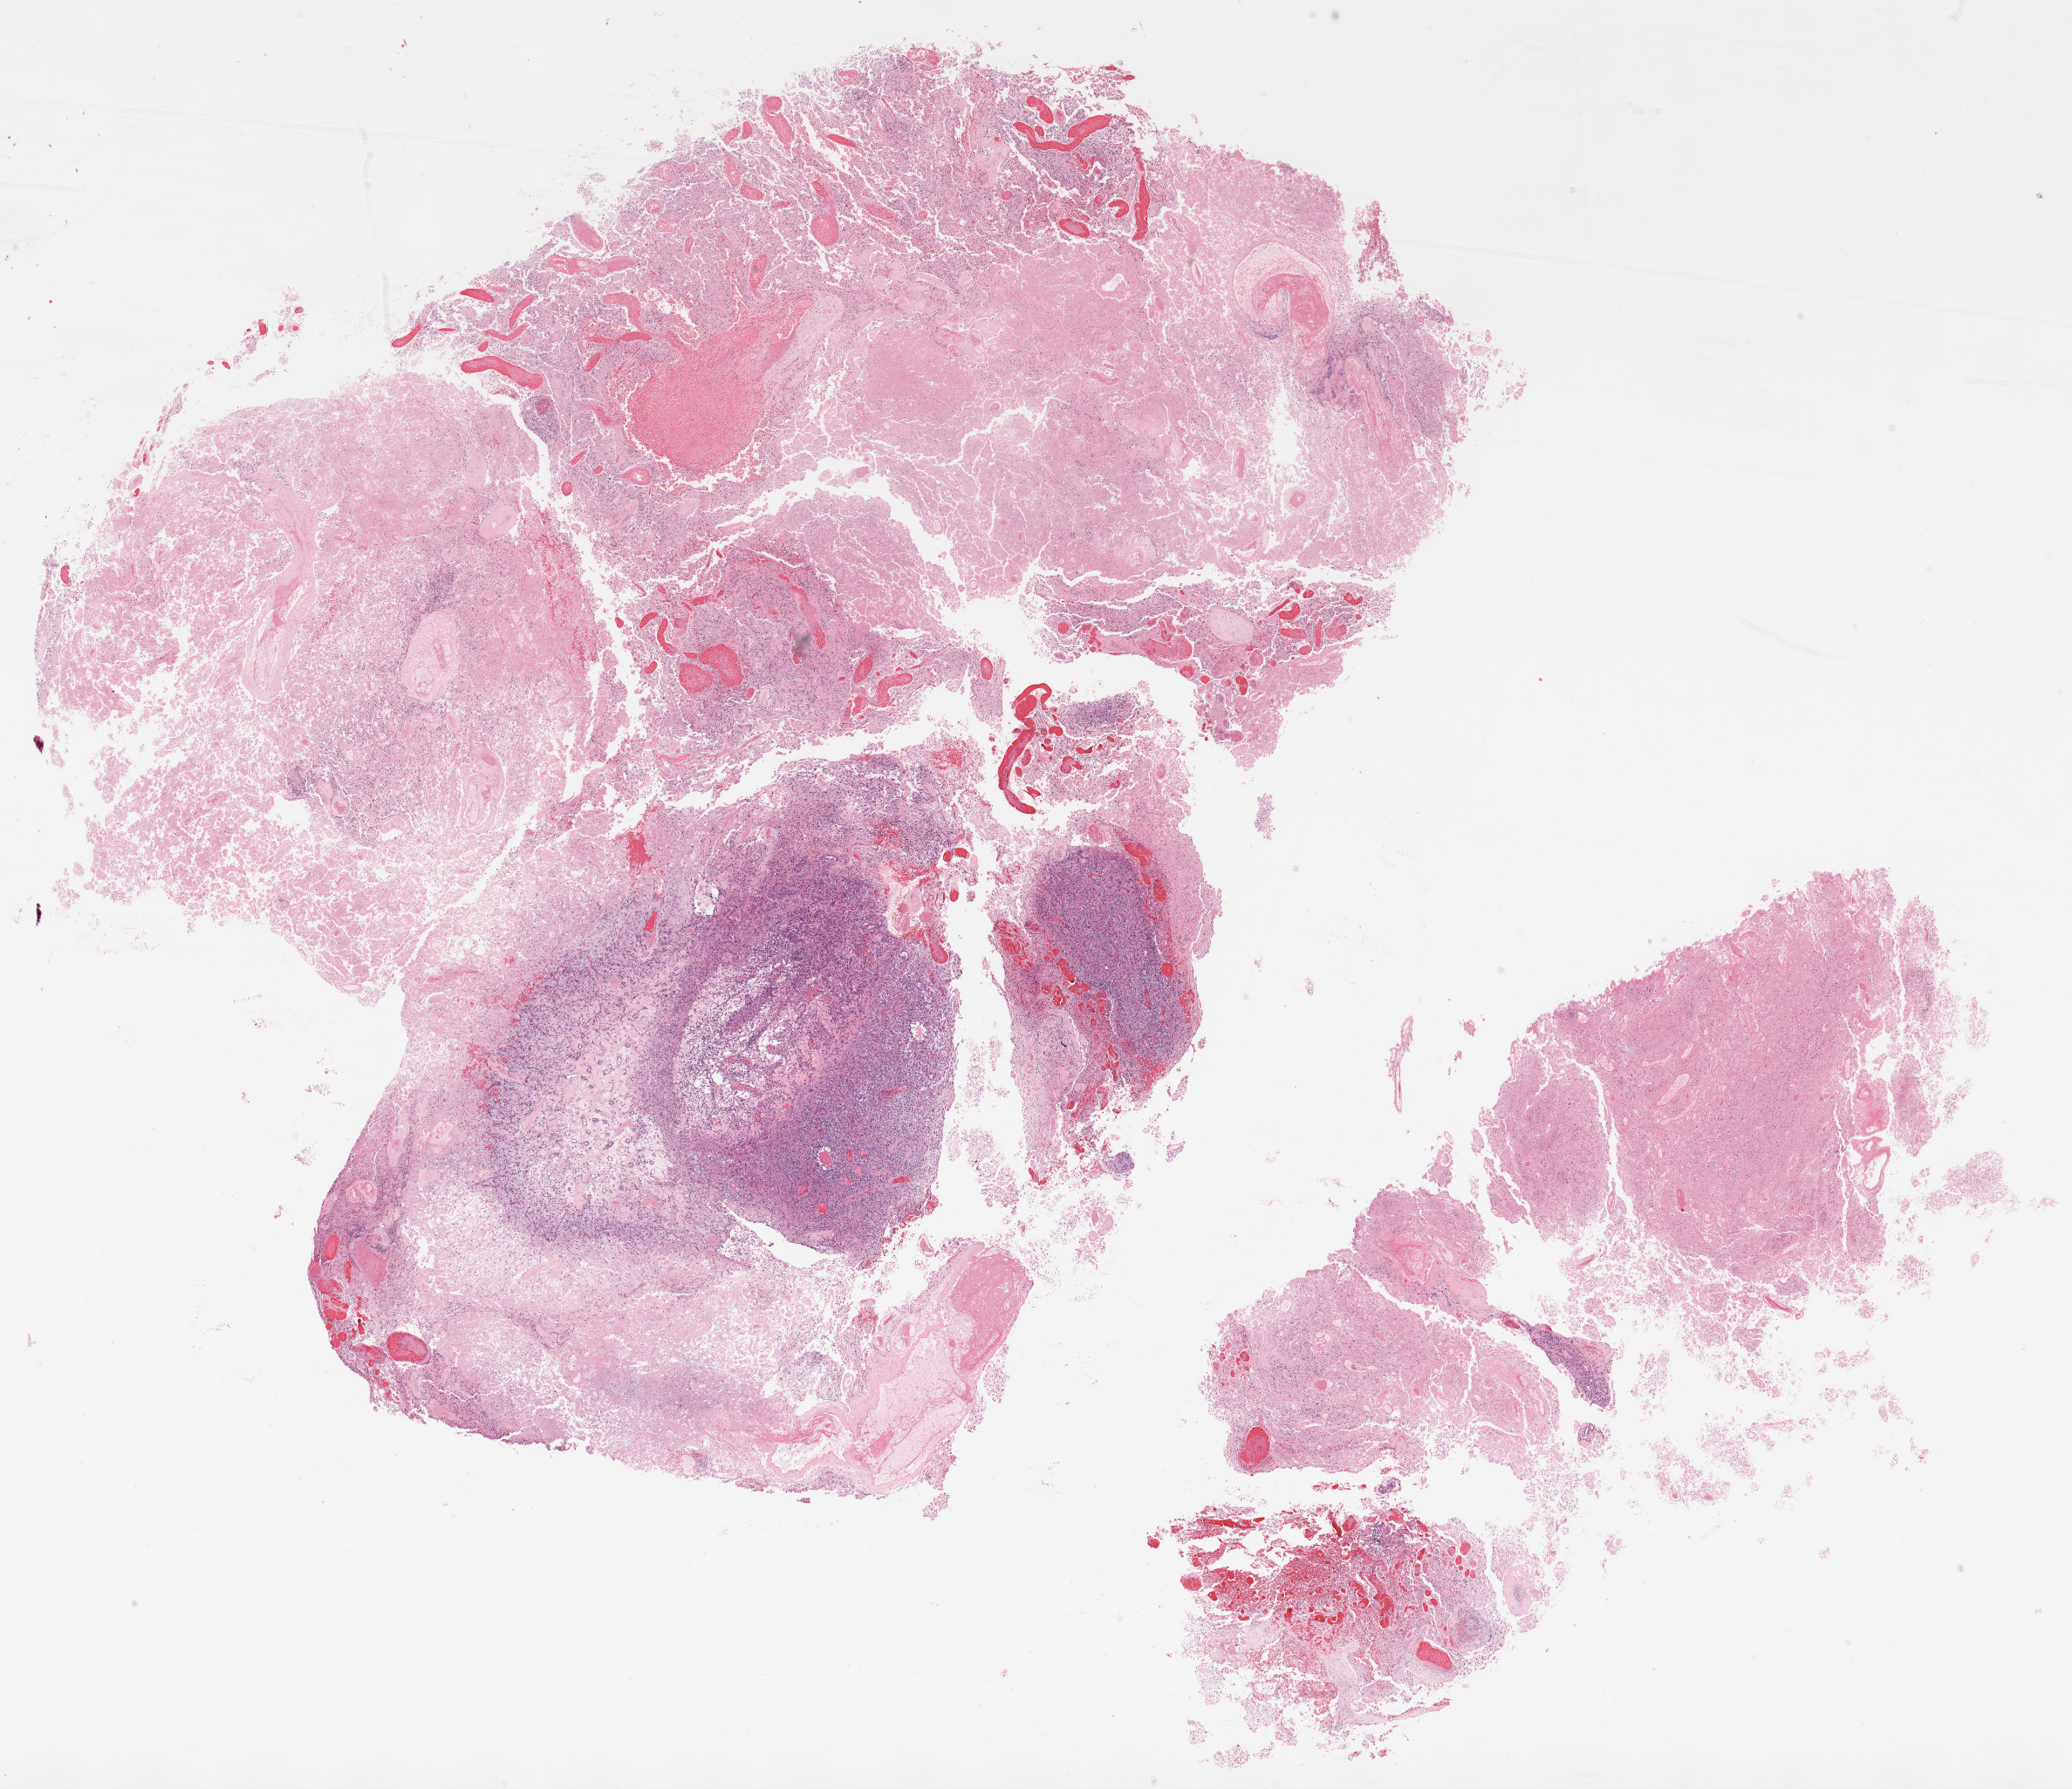
Whole-slide histology image, H&E, low-resolution overview of the scanned area, about 19.1 x 16.5 mm (from a 20x scan); formalin-fixed paraffin-embedded (FFPE) diagnostic section; brain, primary tumour sample. Male, age 39 years at initial diagnosis.
Histologic diagnosis: Glioblastoma.